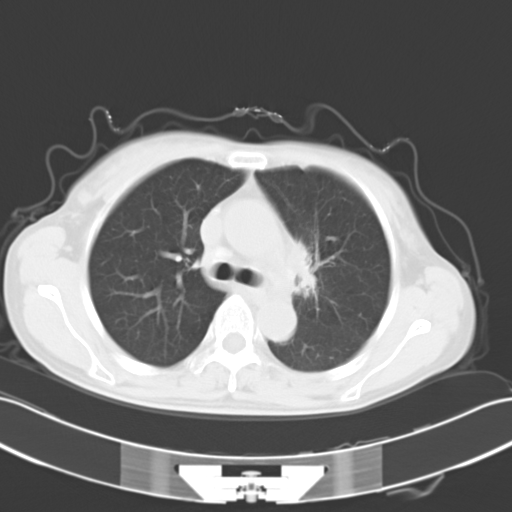
Chest CT, one axial slice; position 19 of 27 along the scan axis; reconstruction kernel B40f; lung window (W 1500 / L -600 HU); 10 mm slice thickness; 512 × 512 image matrix, field of view 353 × 353 mm. Female patient, age 50 years. From the clinical record (not read from this slice): clinical TNM (as recorded): T2a N1 M1c.
Annotated regions visible in this slice (bounding box drawn by a radiologist):
- lung tumour (recorded histology: adenocarcinoma): box from (x=287, y=241) to (x=313, y=292) px